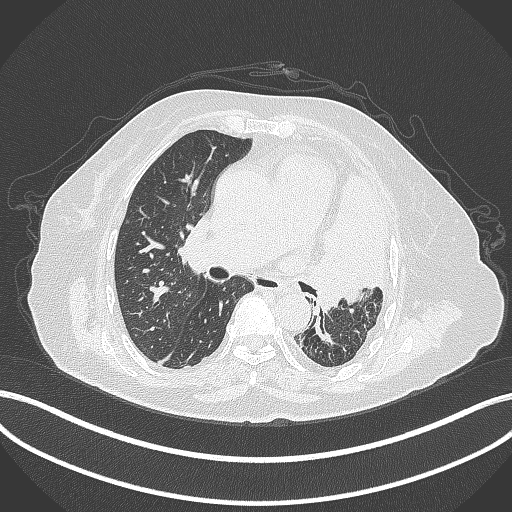
Chest CT, one axial slice. Slice 215 of 399 in the series (ordered by position). Reconstruction kernel B70f. 120 kVp. Lung window (W 1500 / L -600 HU). 512 × 512 image matrix, field of view 400 × 400 mm. Patient: female, 75 years. From the clinical record (not read from this slice): clinical TNM (as recorded): T3 N3 M1.
Structures marked on this image (bounding box drawn by a radiologist):
- lung tumour (recorded histology: adenocarcinoma): bounding box (x1, y1, x2, y2) in pixels: (313, 168, 391, 316)